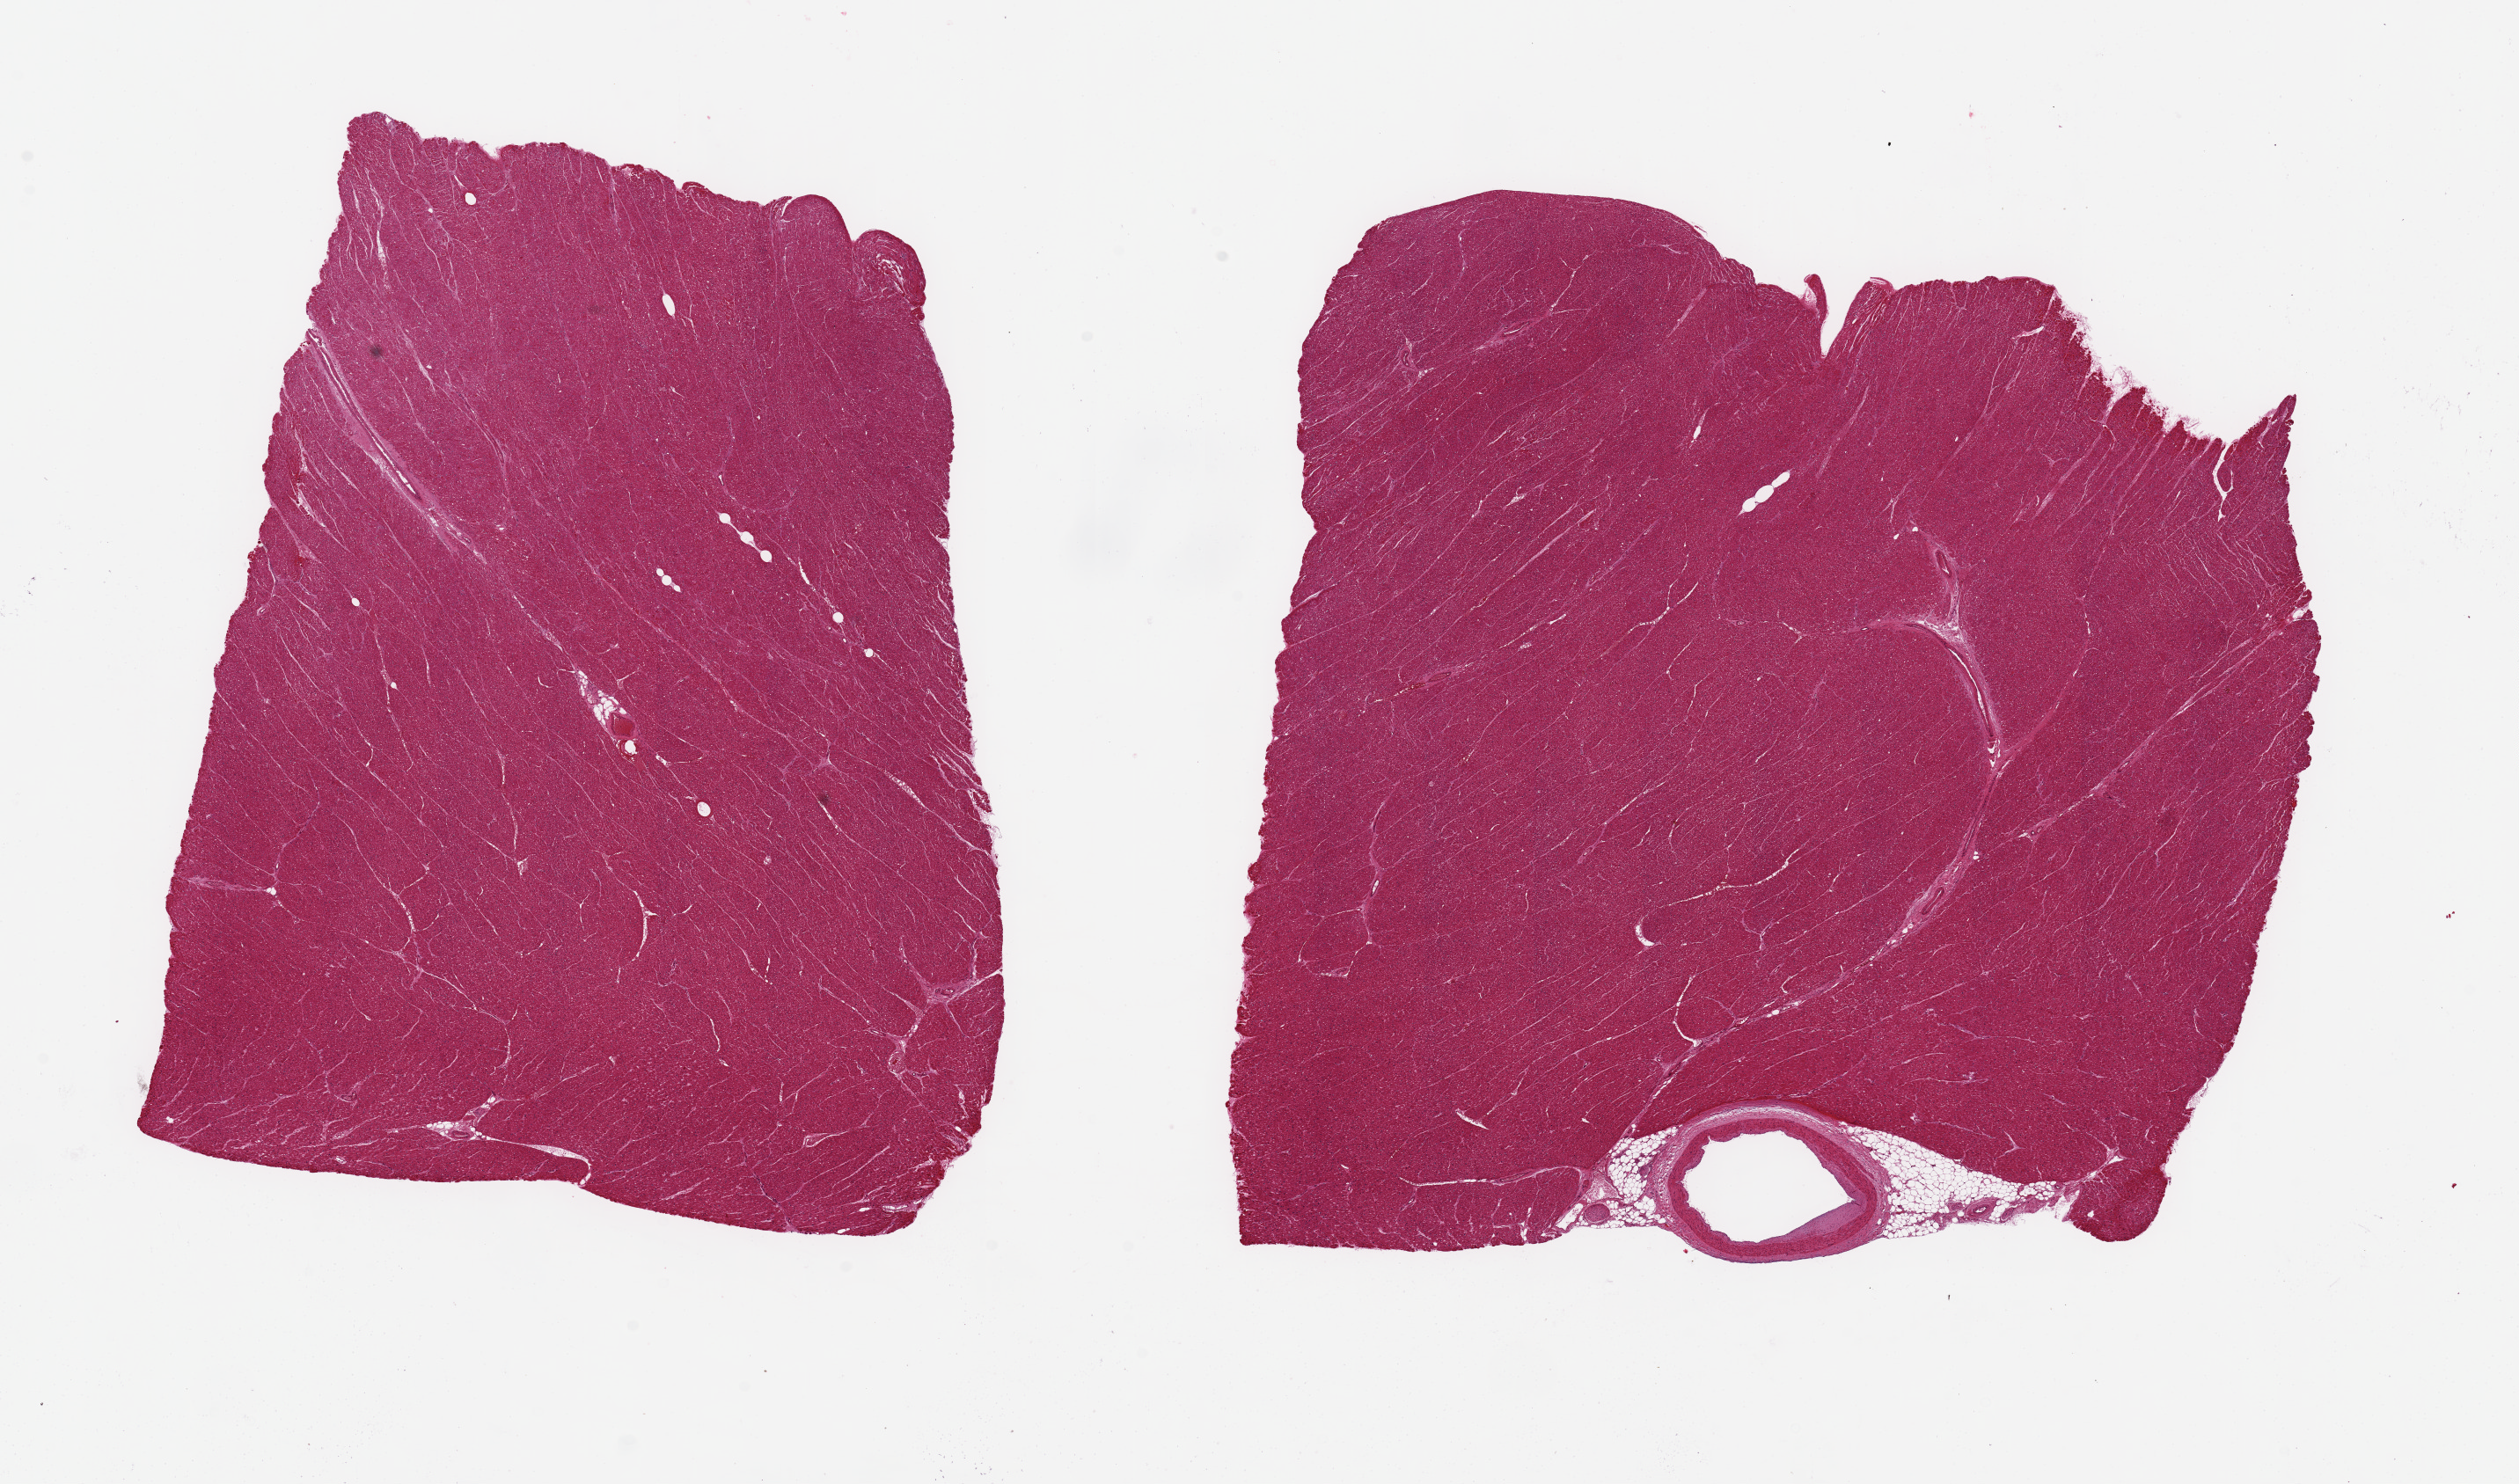
Whole-slide image, hematoxylin and eosin (H&E) stain, shown as a low-resolution overview of the whole scanned area (about 22.6 x 13.3 mm, acquisition: 20x scan), PAXgene-fixed paraffin-embedded (PFPE) section, target tissue: heart, tissue donor sample. Donor sex: female.
Review note (as recorded): 2 pieces, about 9mm; a 2 mm coronary artery is at 1 edge embedded in <5% fat.